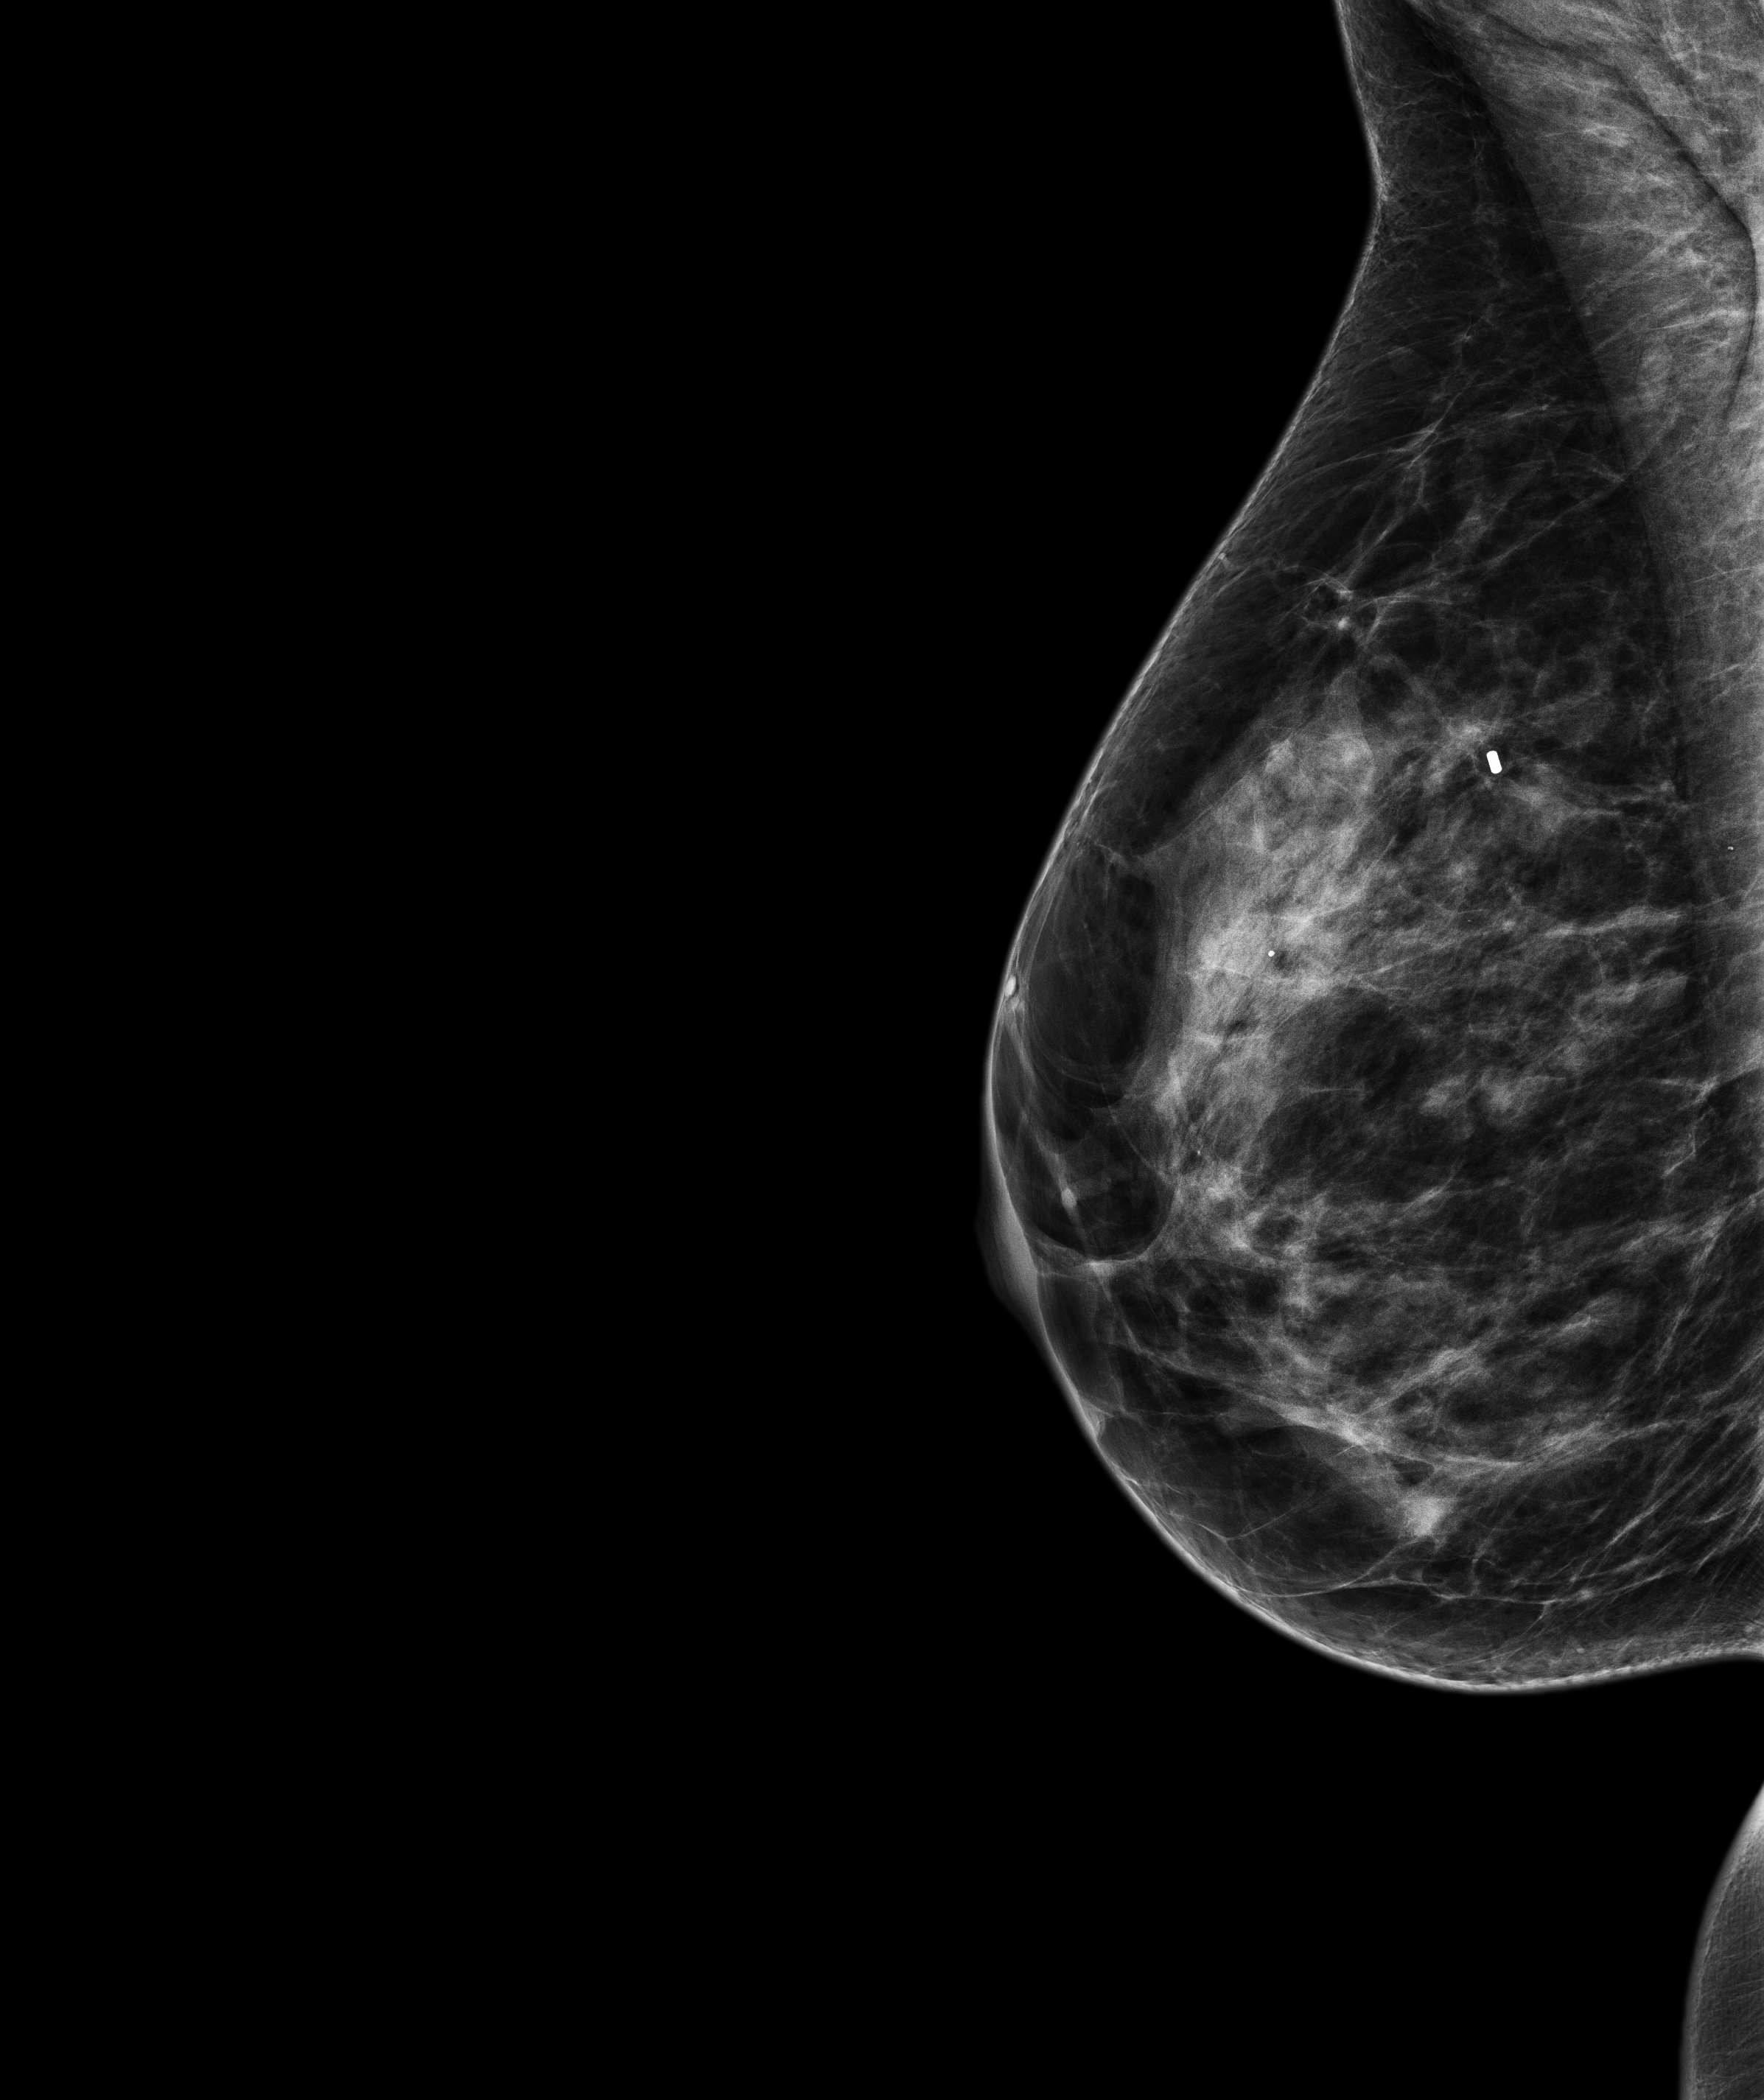
Screening examination; compressed breast thickness 53.8 mm. Patient aged 52 years (female).
Image type: full-field digital mammogram. Breast: right. Projection: medio-lateral oblique projection.